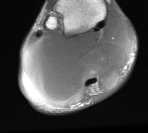
MRI of an extremity soft-tissue mass, one axial slice; position 16 of 76 along the scan axis; MR volume resampled by the dataset authors to the PET/CT grid (not the native acquisition matrix); 3.27 mm slice thickness; 148 × 133 image matrix. Male patient. Case-level facts recorded for this patient, not image findings: histological type: liposarcoma - round cell; grade: high; site of the primary tumour: right calf.
Structures marked on this image (expert contour drawn on MRI and transferred to this co-registered scan by the dataset authors):
- gross tumour volume (mass): bounding box (x1, y1, x2, y2) in pixels: (24, 19, 130, 106)